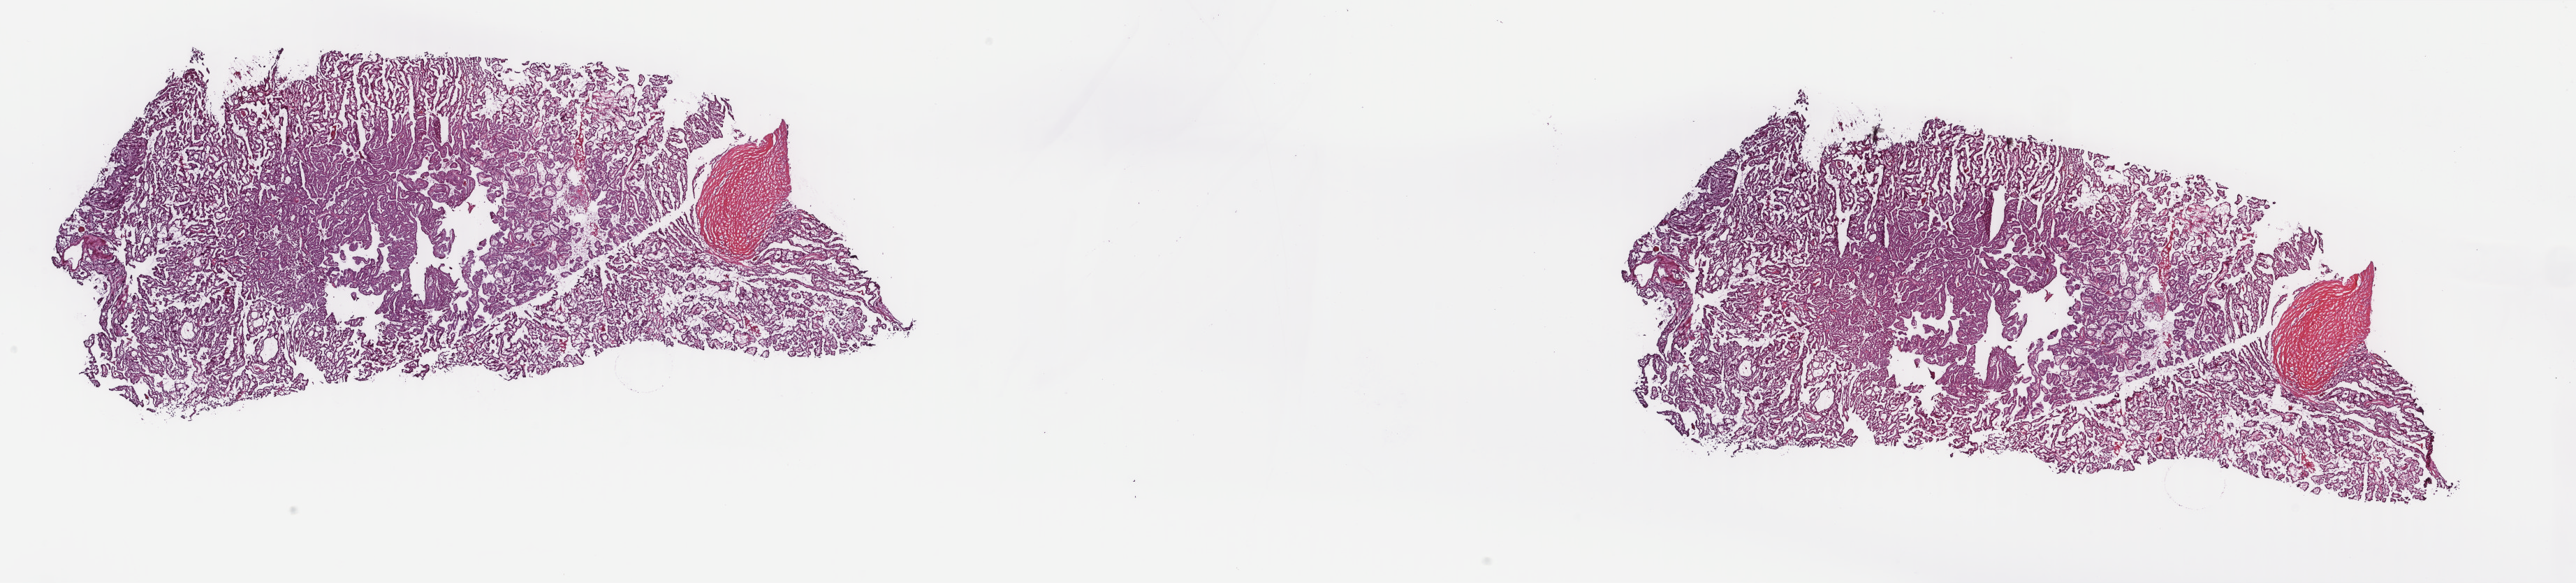
H&E-stained whole-slide image — a low-resolution overview of the entire scanned area, about 29.3 x 6.6 mm. Frozen section. Sample: primary tumour, thyroid. Female, age 44 years at initial diagnosis. Composition of this section per pathologist review: tumour cells 90%, tumour nuclei 100%, normal cells 0%, stromal cells 10%, necrosis 0%. Inflammatory infiltration, as recorded: lymphocyte infiltration 0%, monocyte infiltration 2%, neutrophil infiltration 0%.
TNM: T3 N0 M0. AJCC pathologic stage: III (7th edition). Histologic diagnosis: Papillary carcinoma, columnar cell (thyroid gland). Laterality: right. Lymph nodes positive (case pathology): 0 of 2 examined.